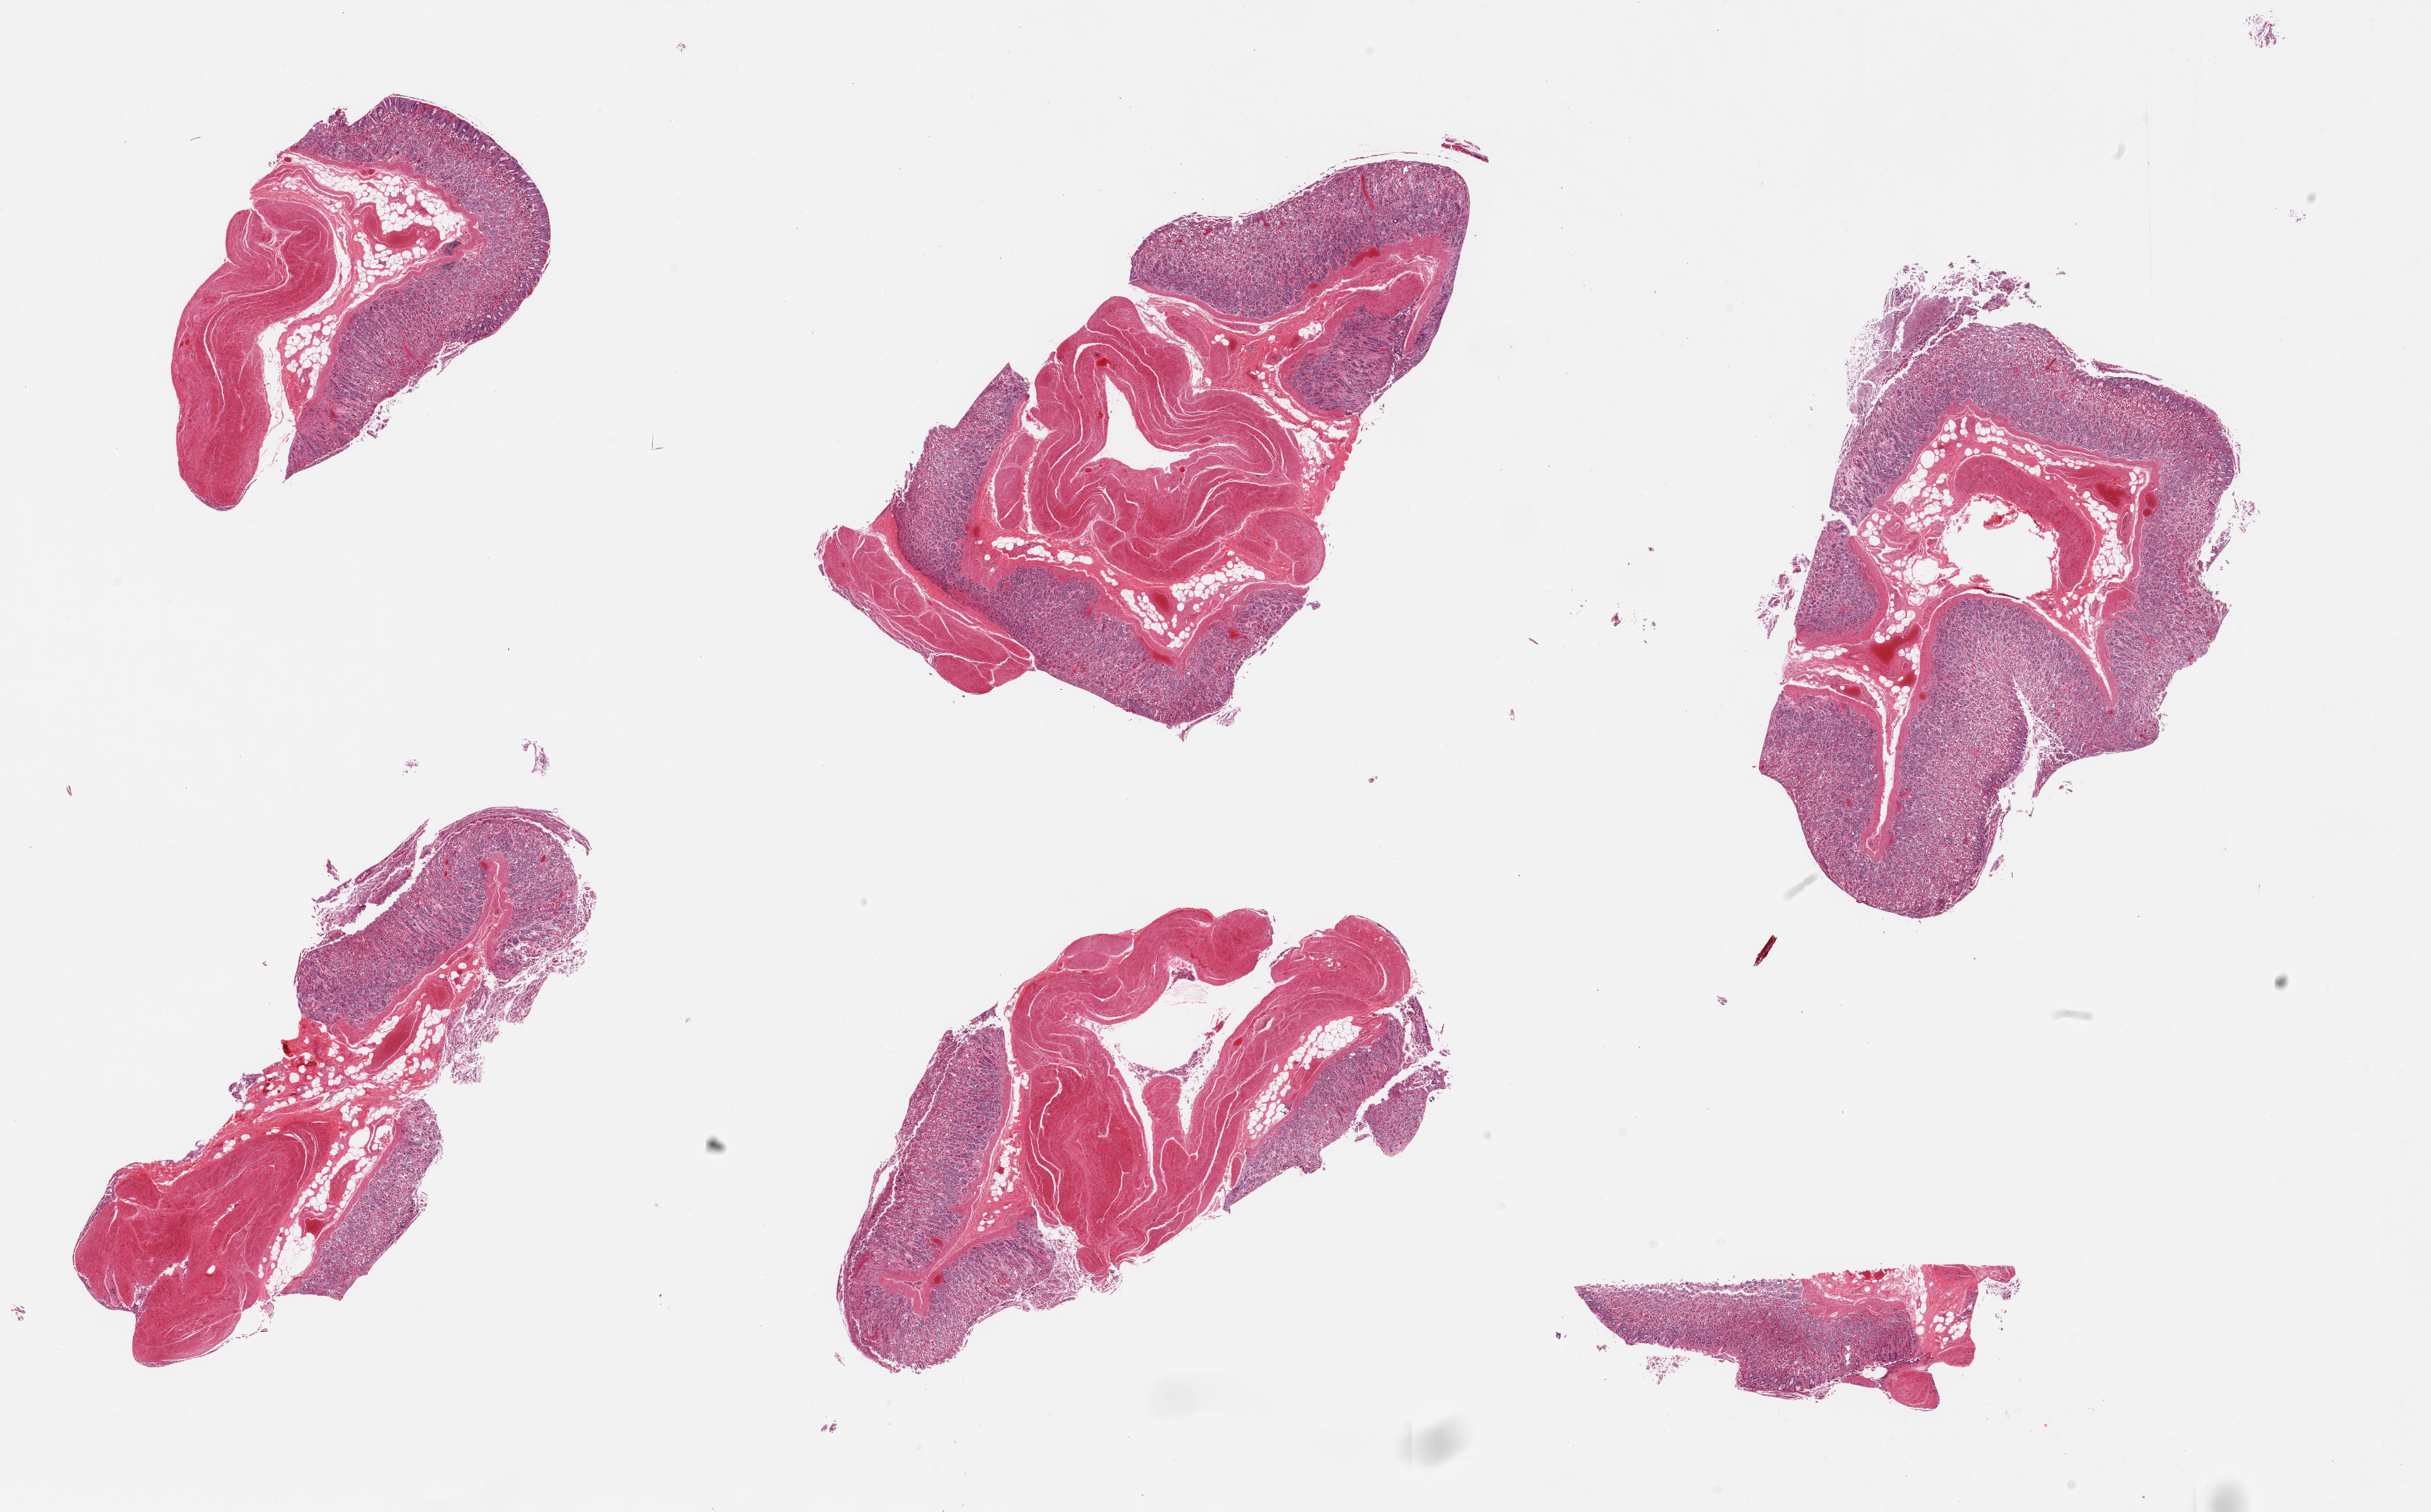
Hematoxylin and eosin (H&E) whole-slide image — whole scanned area (about 30.5 x 19.0 mm) shown as a low-resolution overview. PAXgene-fixed paraffin-embedded (PFPE) section. Section of stomach (target tissue). Donor tissue sample. Donor: female.
Pathologist's review note for this sample: 6 pieces, mucosa, submucosa, and muscularis.